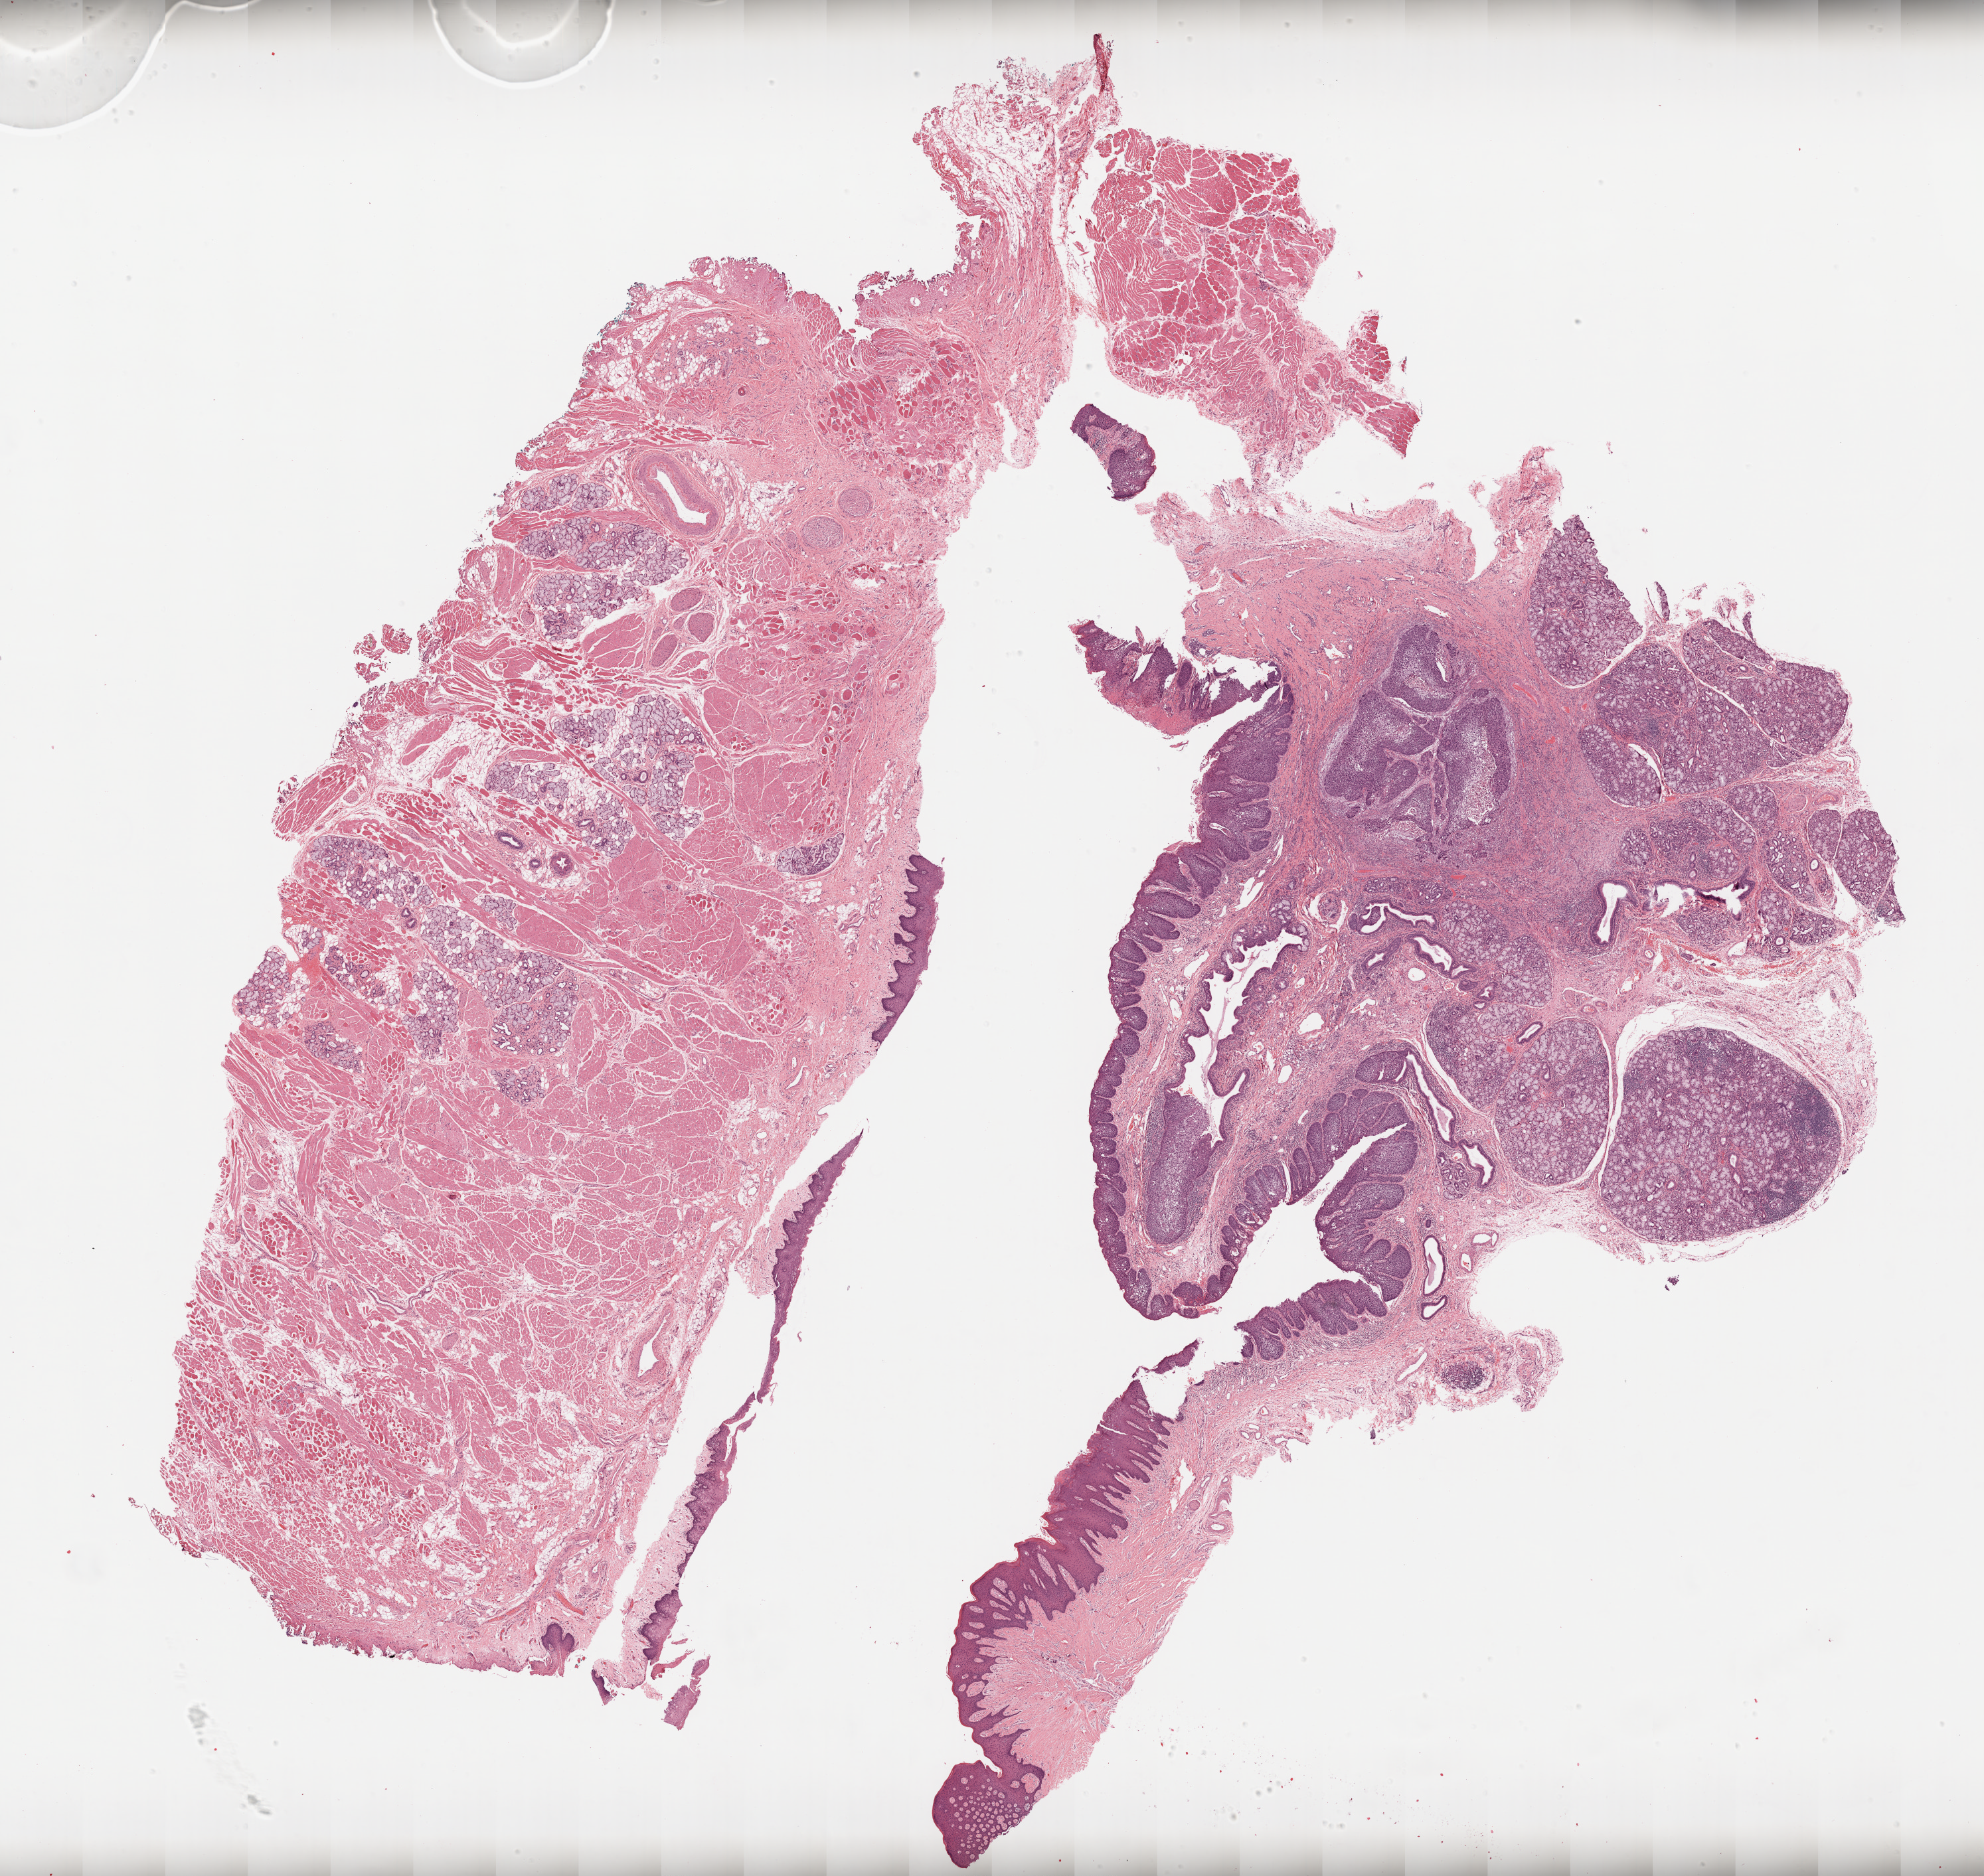
Digitized Hematoxylin and eosin (H&E) stained tissue section (whole slide) — shown as a low-resolution overview of the whole scanned area (about 24.0 x 22.7 mm, from a 20x scan), FFPE section, primary tumour sample from the head and neck. Male patient; age at initial diagnosis 56 years. Histologic grade: G2 (moderately differentiated).
Pathologic diagnosis: Squamous cell carcinoma, NOS. Laterality: midline. AJCC pathologic stage: III.